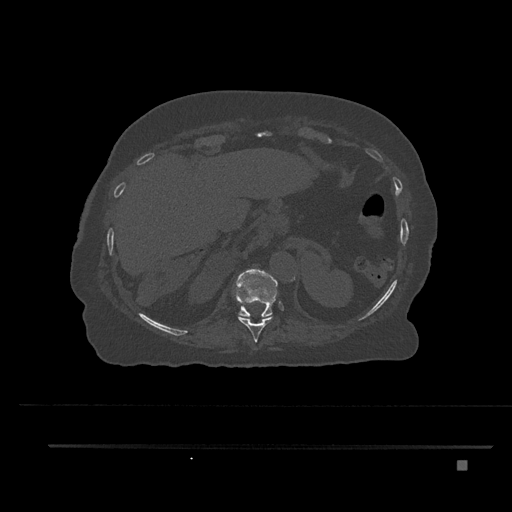
CT including the spine, one axial slice; slice 336 of 797 in the series (ordered by position); reconstruction kernel Br40s/3; 120 kVp; bone window (W 1800 / L 400 HU); 0.5 mm slice thickness; 512 × 512 image matrix. Female patient, age 76 years. From the clinical record (not read from this slice): primary cancer: lung; vertebrae with lytic lesions (as recorded): T11, L3.
Structures marked on this image (semi-automatic segmentation, software-assisted and operator-edited):
- T10 vertebra: bounding box <233,286,273,342> (left, top, right, bottom; pixels)
- T11 vertebra: <236,269,278,317>